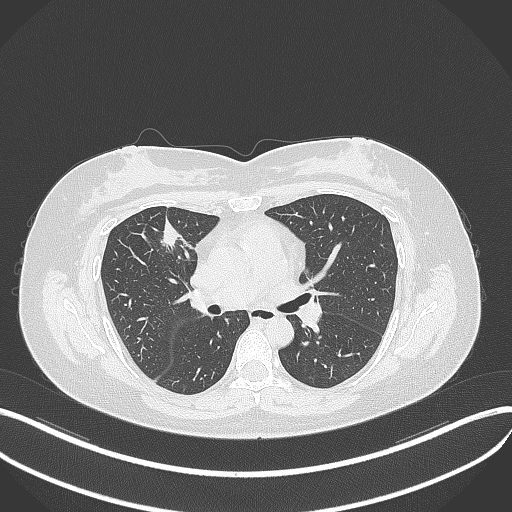
Chest CT, one axial slice. Slice 183 of 273 in the series (ordered by position). Reconstruction kernel B70f. Lung window (W 1500 / L -600 HU). 512 × 512 image matrix, field of view 400 × 400 mm. Patient: female, 42 years. From the clinical record (not read from this slice): clinical TNM (as recorded): T1b N0 M0.
Outlined on this slice (bounding box drawn by a radiologist):
- lung tumour (recorded histology: adenocarcinoma): box from (x=156, y=214) to (x=187, y=250) px